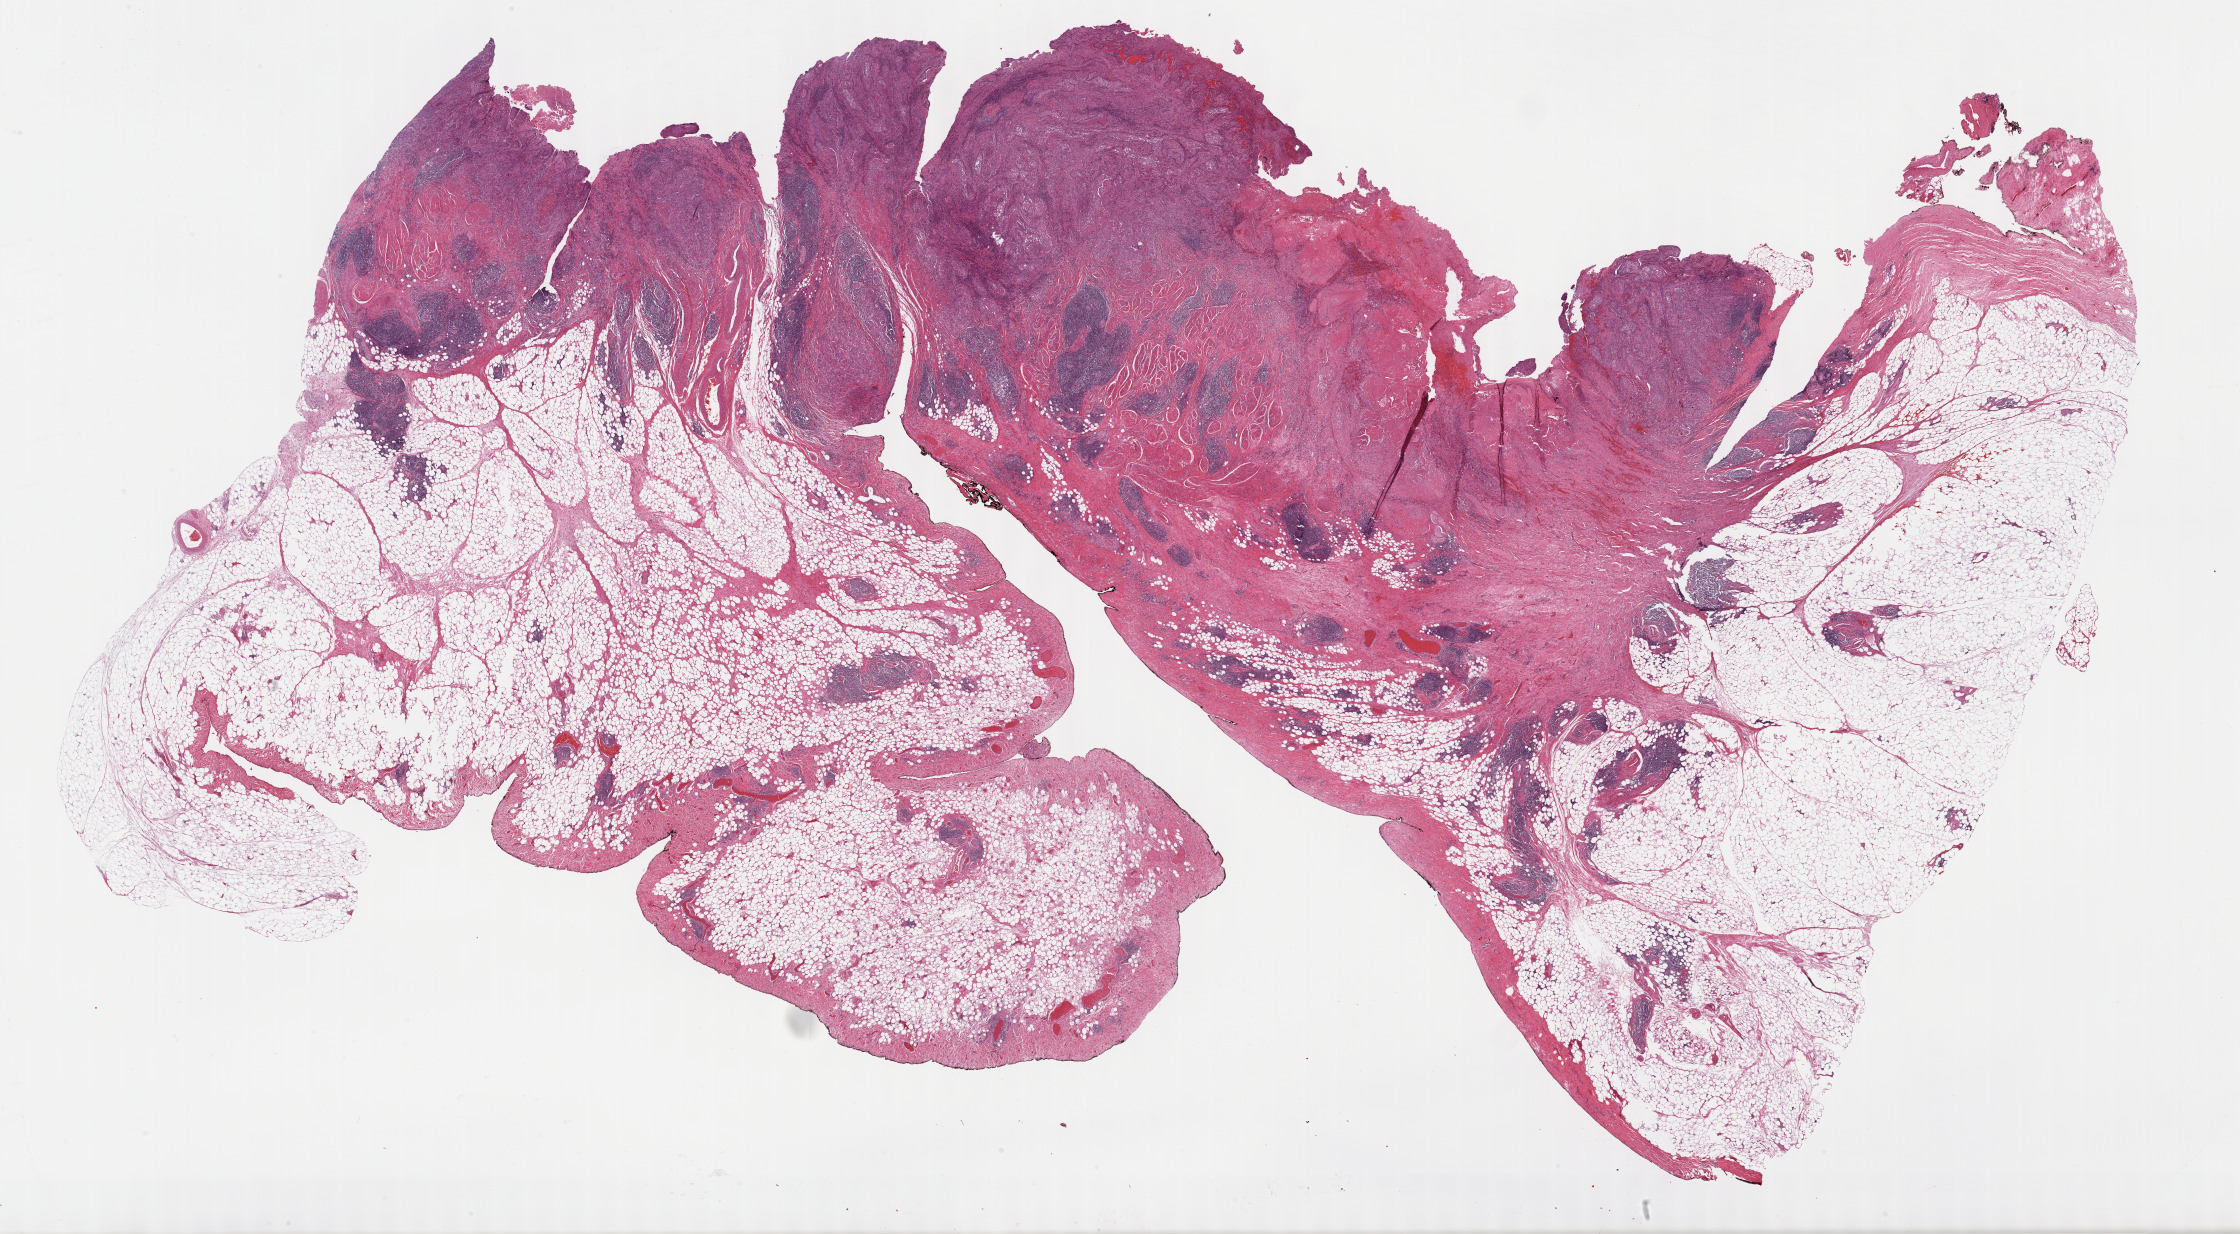
Digitized H&E-stained tissue section (whole slide), a low-resolution overview of the entire scanned area, about 36.2 x 20.0 mm (acquisition: 40x scan). Formalin-fixed paraffin-embedded (FFPE) diagnostic section. Bladder, primary tumour sample. Female, age 76 years at initial diagnosis. Histologic grade: high grade.
AJCC pathologic stage: II (7th edition). Pathologic diagnosis: Transitional cell carcinoma (lateral wall of bladder).